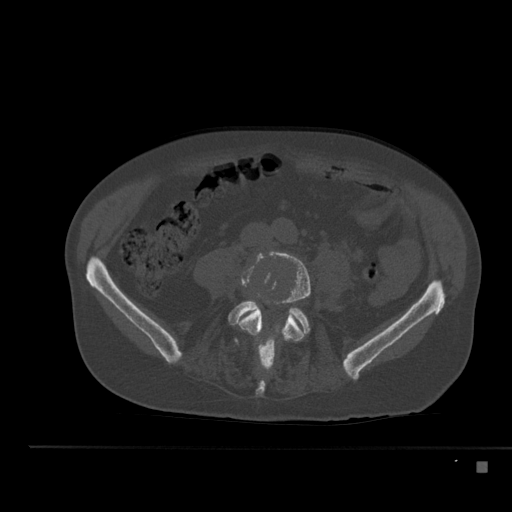
CT including the spine, one axial slice; position 136 of 517 along the scan axis; reconstruction kernel Br40s; 120 kVp; bone window (W 1800 / L 400 HU); 512 × 512 image matrix. Male patient, age 70 years. From the clinical record (not read from this slice): primary cancer: renal; vertebrae with lytic lesions (as recorded): T4, T6, T10, T12, L3, L4, L5.
Annotated regions visible in this slice (semi-automatic segmentation, software-assisted and operator-edited):
- L4 vertebra: bounding box (x1, y1, x2, y2) in pixels: (238, 251, 311, 371)
- L5 vertebra: (228, 301, 310, 394)